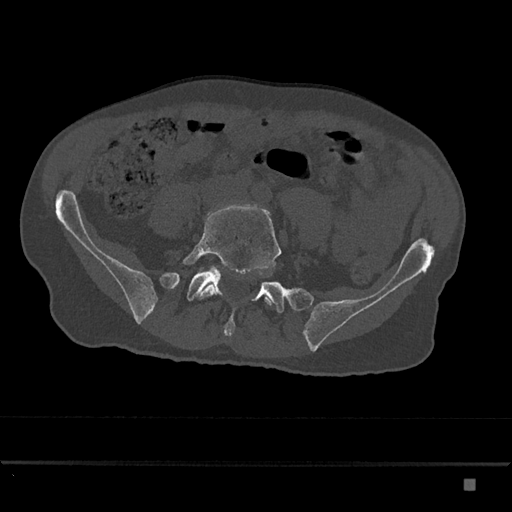
CT including the spine, one axial slice; slice 261 of 797 in the series (ordered by position); 120 kVp; bone window (W 1800 / L 400 HU); 0.5 mm slice thickness; 512 × 512 image matrix, field of view 390 × 390 mm. Patient: male, 72 years. From the clinical record (not read from this slice): primary cancer: prostate.
Outlined on this slice (semi-automatically segmented with operator editing):
- L5 vertebra: box from (x=183, y=206) to (x=282, y=306) px